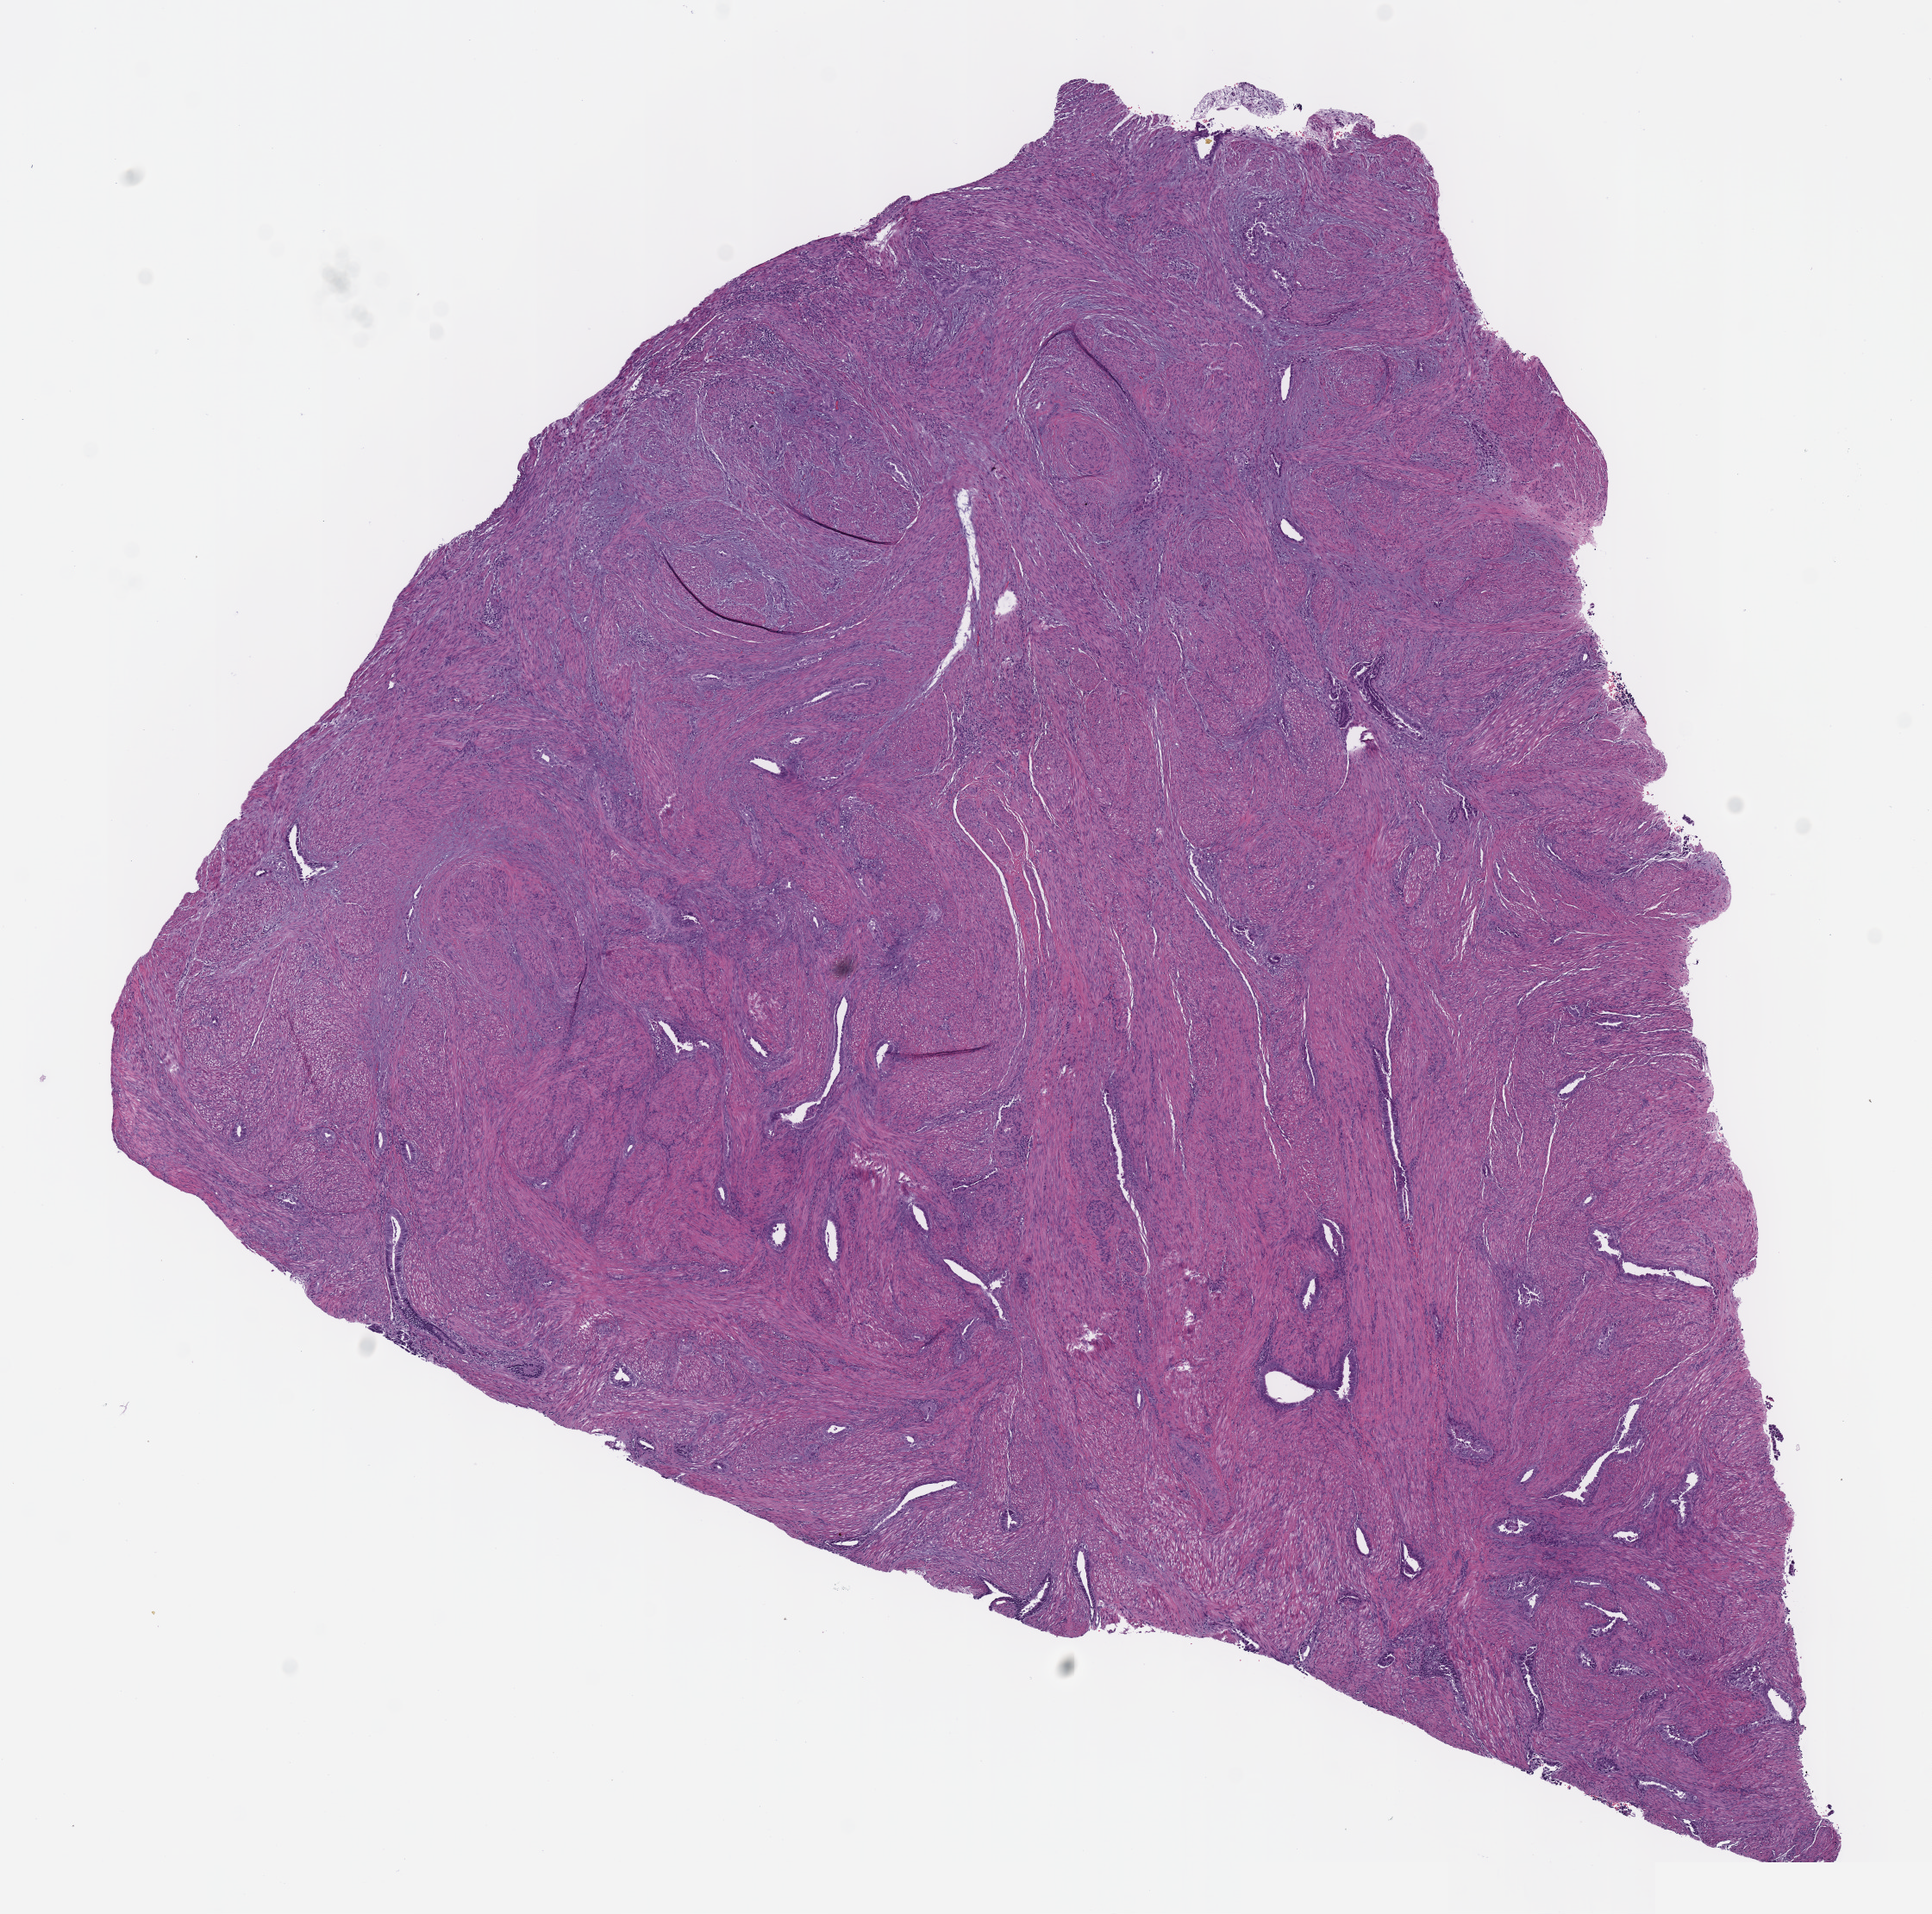
Whole-slide histology image, H&E-stained — shown as a low-resolution overview of the whole scanned area (about 8.8 x 8.7 mm, from a 40x scan), formalin-fixed paraffin-embedded (FFPE) diagnostic section, uterus, primary tumour sample. Female patient; age at initial diagnosis 60 years. Histologic grade: G3 (poorly differentiated).
Pathologic diagnosis: Serous cystadenocarcinoma, NOS (endometrium). FIGO stage: IIIC. Lymph nodes positive (case pathology): 0 of 9 examined.